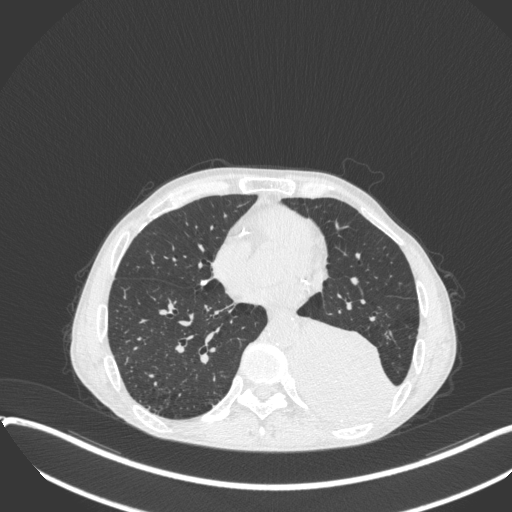
Chest CT, one axial slice. Slice 138 of 400 in the series (ordered by position). Reconstruction kernel B31f. 120 kVp. Lung window (W 1500 / L -600 HU). 1 mm slice thickness. 512 × 512 image matrix. Male patient, age 57 years. From the clinical record (not read from this slice): clinical TNM (as recorded): T4 N0 M0.
Outlined on this slice (rectangle marked by the reading radiologist):
- lung tumour (recorded histology: squamous cell carcinoma): bounding box [x1, y1, x2, y2] px = [289, 311, 395, 425]